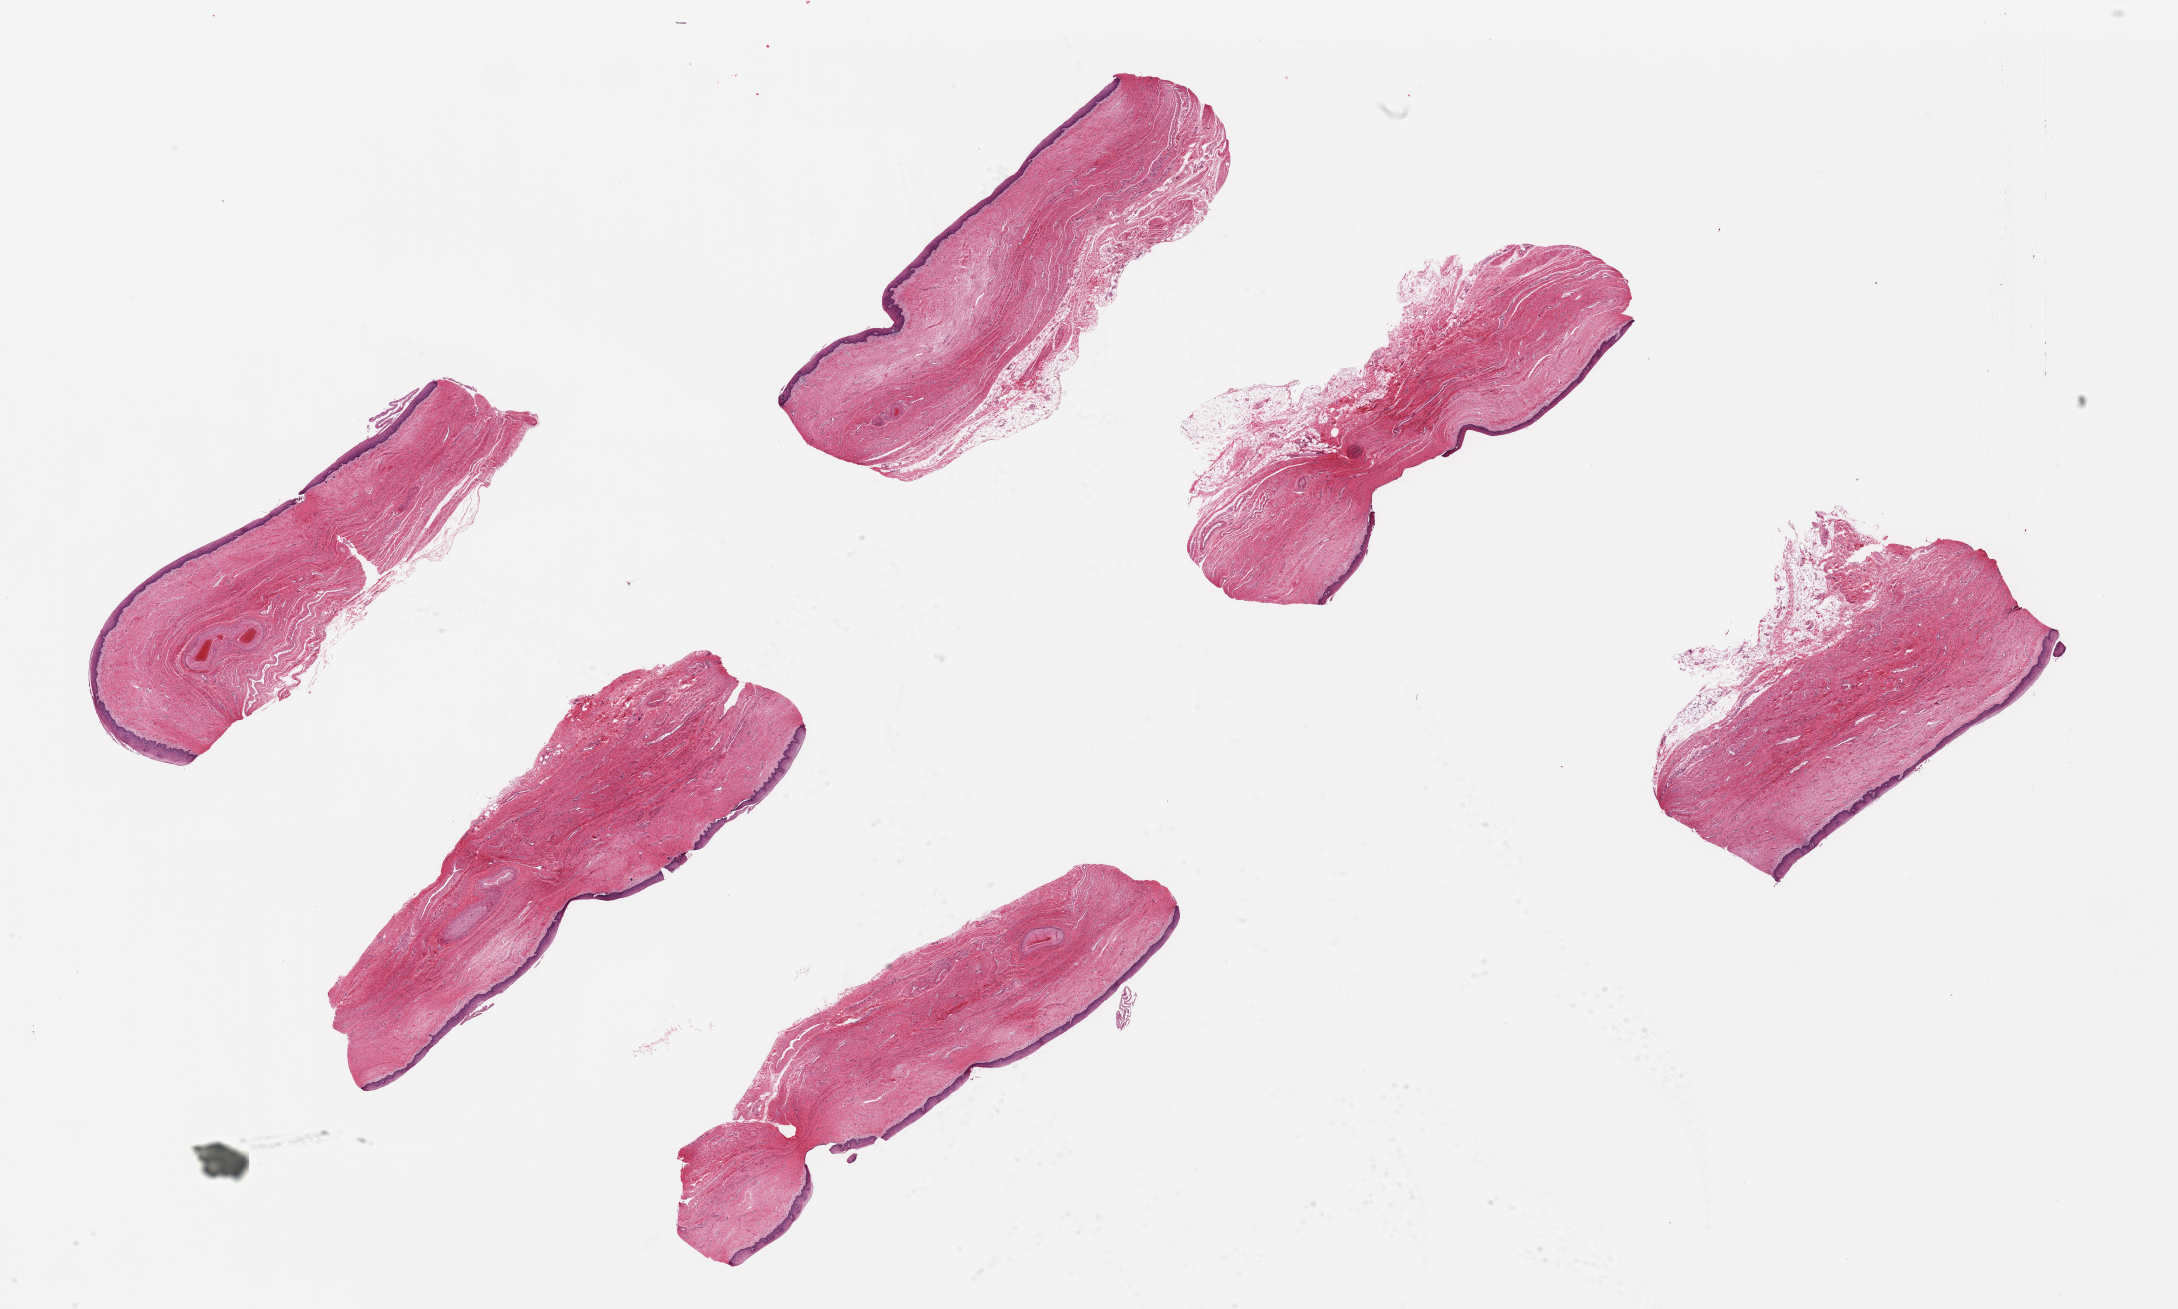
Whole-slide image, haematoxylin and eosin stain, whole scanned area (about 34.5 x 20.7 mm, from a 20x scan) shown as a low-resolution overview, PAXgene-fixed paraffin-embedded (PFPE) section, section of vagina (target tissue), donor tissue sample. Female donor.
Review note (as recorded): 6 ~8x3 mm pieces; well preserved squamous epithelium 0.13 mm thick.